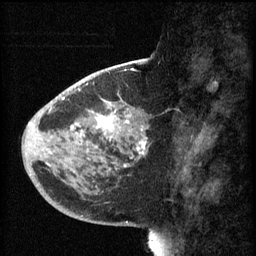
Breast MRI (dynamic contrast-enhanced), one sagittal slice. Position 24 of 60 along the scan axis. 3 images stored at this slice position (order not interpretable as contrast timing). 1.5 T. TE 4.2 ms, TR 8.1 ms. 2 mm slice thickness. 256 × 256 image matrix. Female patient, age 44 years.
Outlined on this slice (semi-automatically segmented with operator editing):
- analysis volume of interest (the breast-tissue region the enhancement analysis was run in; not a lesion): bounding box (x1, y1, x2, y2) in pixels: (59, 110, 149, 169)
- tumour enhancement mask (voxels above the 70 % enhancement threshold inside the analysis volume of interest): (75, 110, 147, 167)